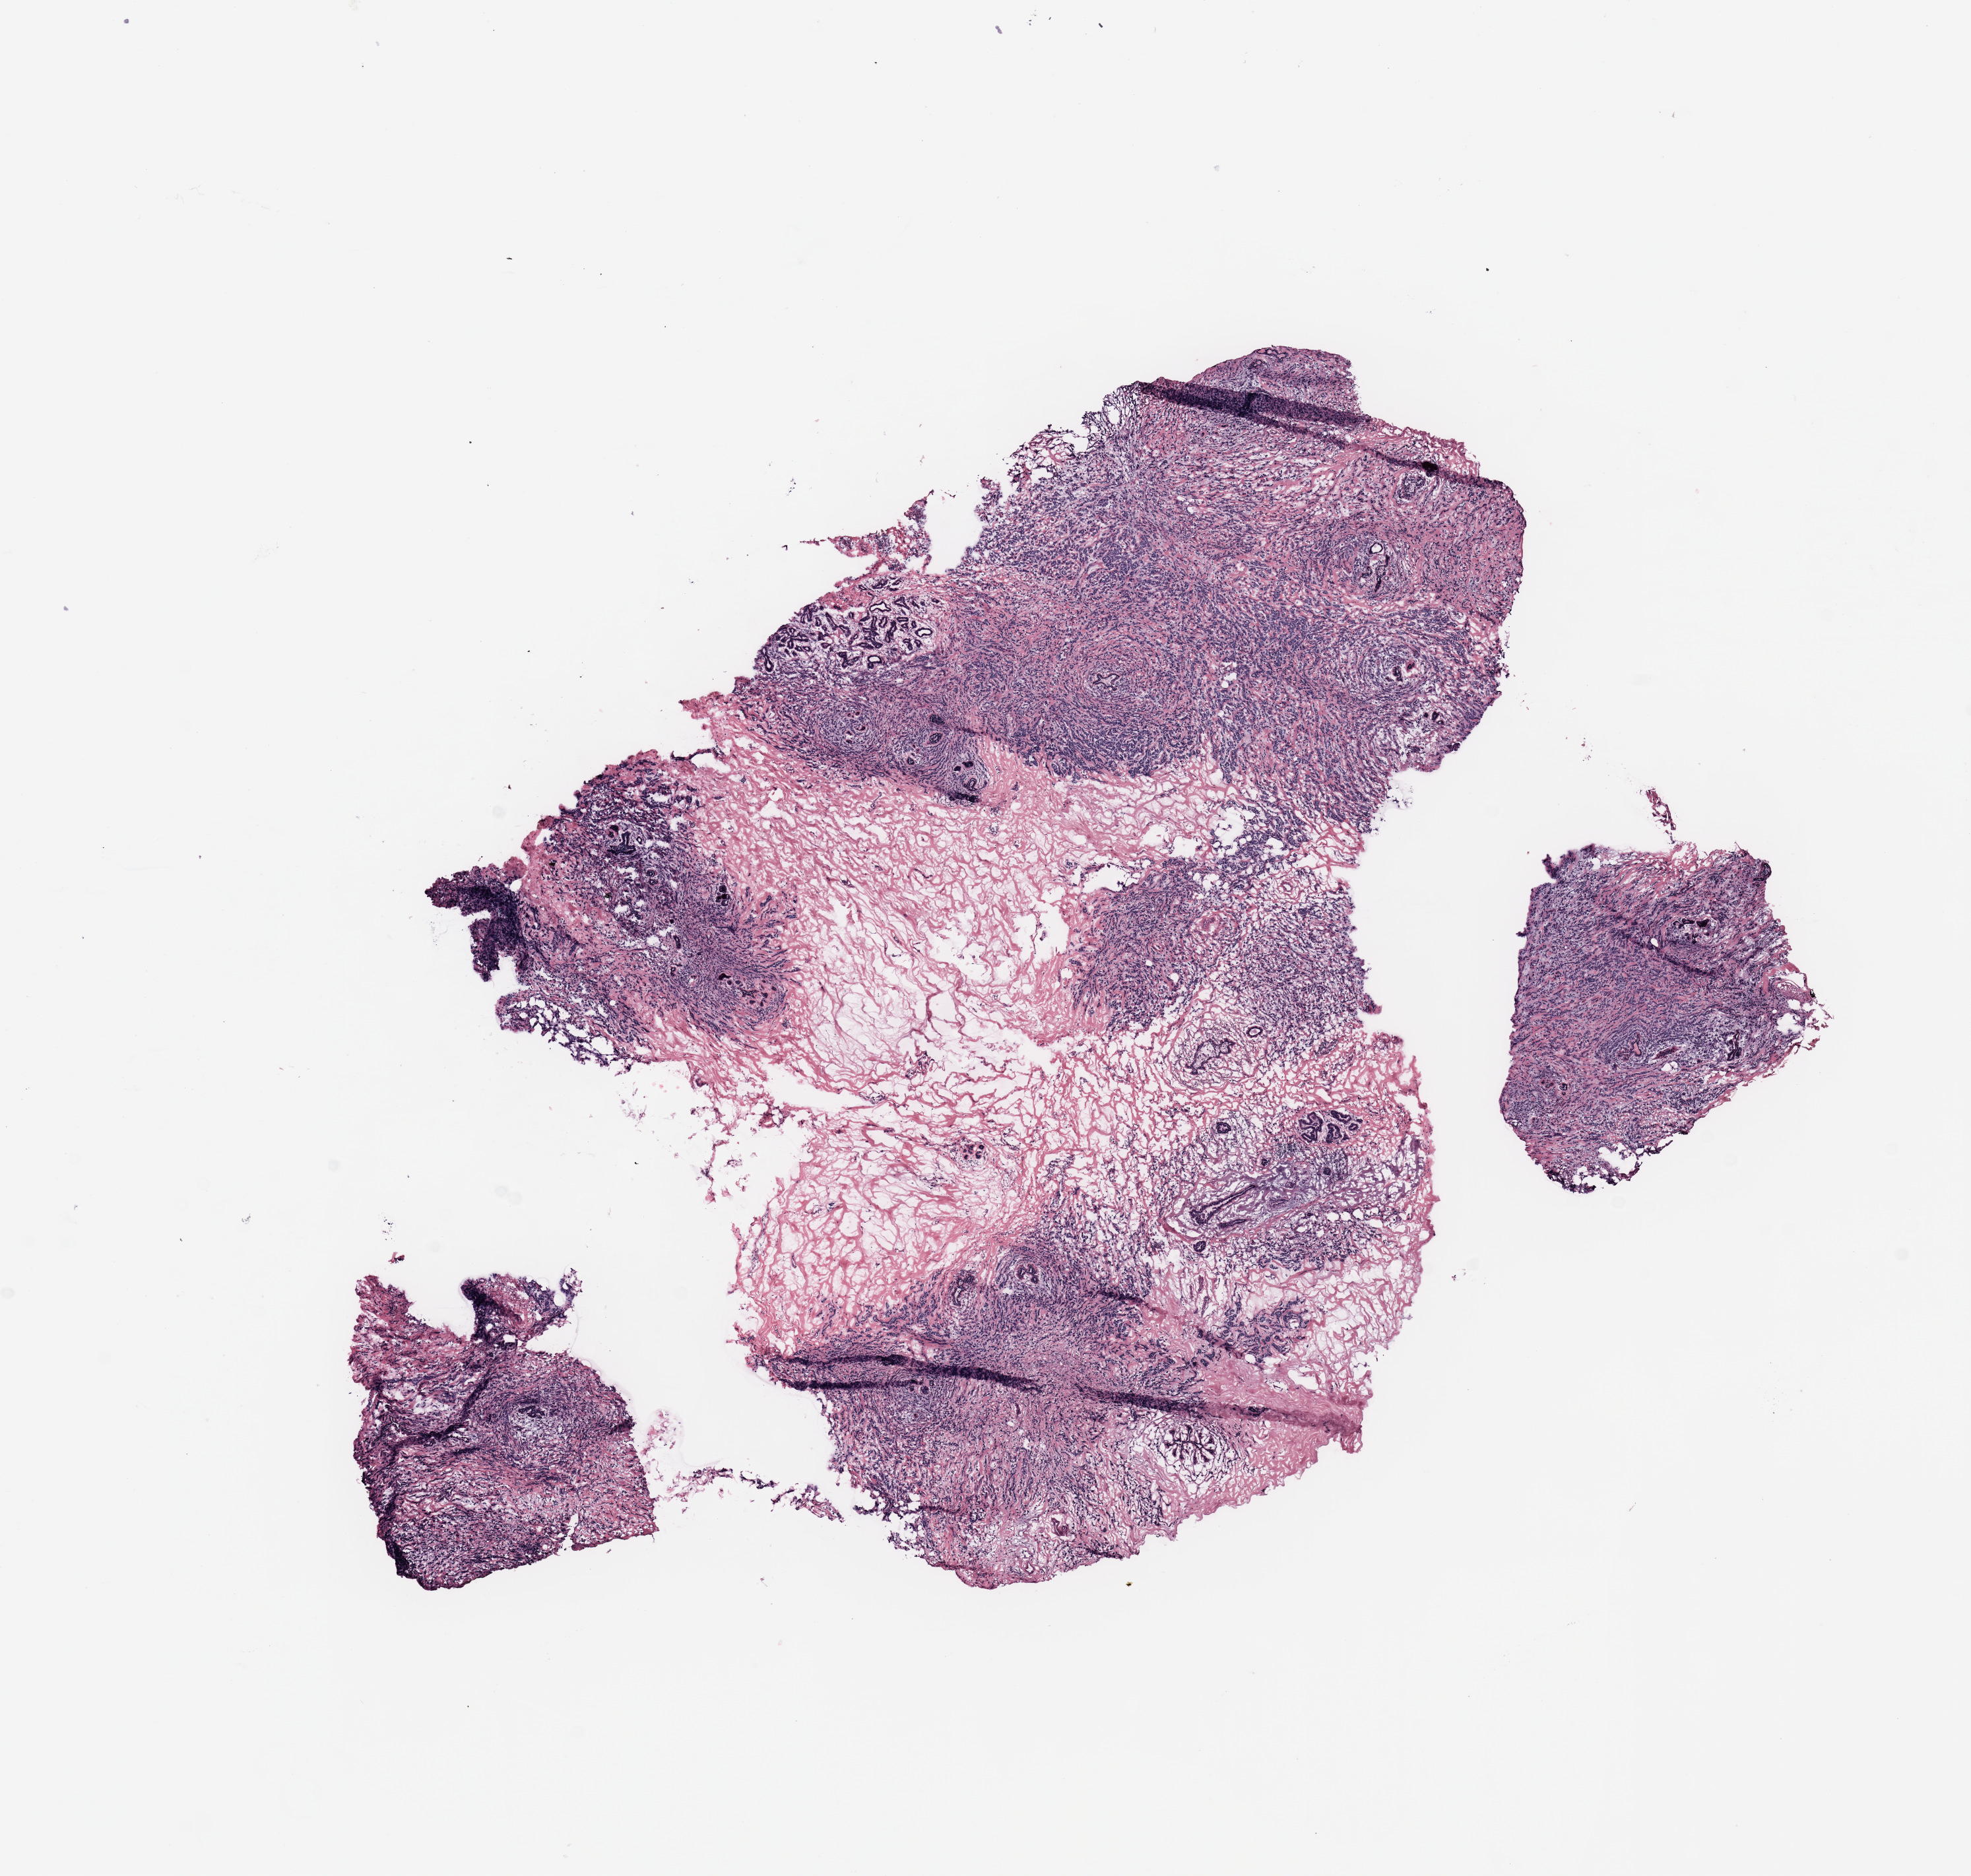
Hematoxylin and eosin (H&E) stained whole-slide image — whole scanned area (about 11.8 x 11.2 mm) shown as a low-resolution overview. 46-year-old female patient.
Specimen: tumour tissue sample, breast.